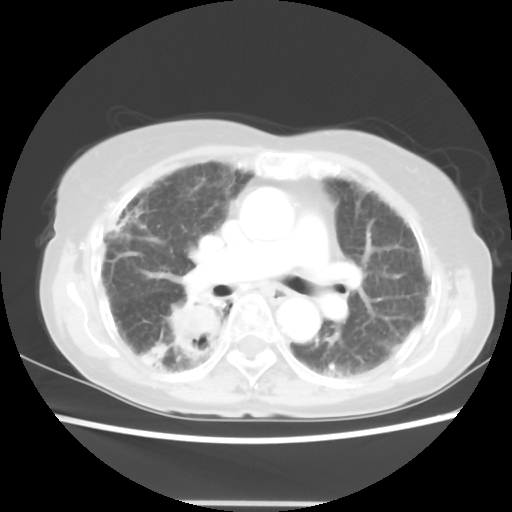
Chest CT, one axial slice; position 31 of 52 along the scan axis; reconstruction kernel STANDARD; lung window (W 1500 / L -600 HU); 5 mm slice thickness; 512 × 512 image matrix, field of view 325 × 325 mm. Patient: female, 71 years. Case-level facts recorded for this patient, not image findings: clinical TNM (as recorded): T3 N0 M0.
Structures marked on this image (bounding box drawn by a radiologist):
- lung tumour (recorded histology: squamous cell carcinoma): bounding box (x1, y1, x2, y2) in pixels: (167, 300, 222, 360)